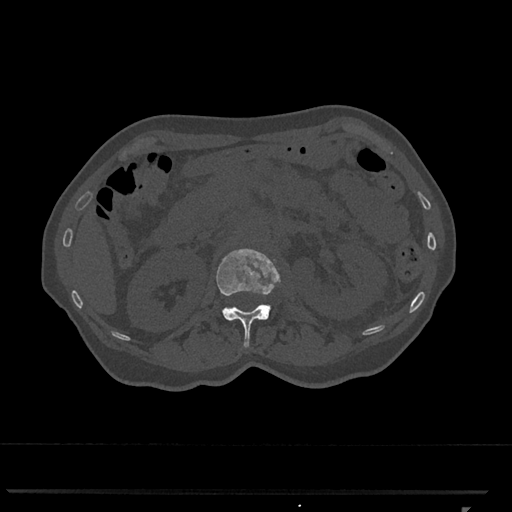
CT including the spine, one axial slice; slice 395 of 793 in the series (ordered by position); reconstruction kernel Br40s/3; bone window (W 1800 / L 400 HU); 0.5 mm slice thickness; 512 × 512 image matrix, field of view 380 × 380 mm. Female patient, age 62 years. From the clinical record (not read from this slice): primary cancer: renal.
Annotated regions visible in this slice (semi-automatically segmented with operator editing):
- L1 vertebra: bounding box <216,249,281,348> (left, top, right, bottom; pixels)